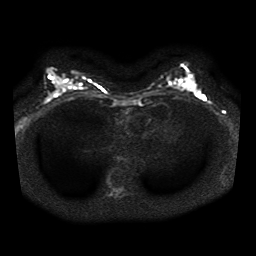
Breast MRI, one axial slice. Position 20 of 41 along the scan axis. Diffusion-weighted series; image 2 of 4 stored at this slice position (different b-values; order by instance number). 1.5 T. 5 mm slice thickness. 256 × 256 image matrix, field of view 320 × 320 mm. Female patient.
Structures marked on this image (manually delineated by an expert):
- tumour on diffusion-weighted imaging: bounding box [x1, y1, x2, y2] px = [187, 80, 196, 89]